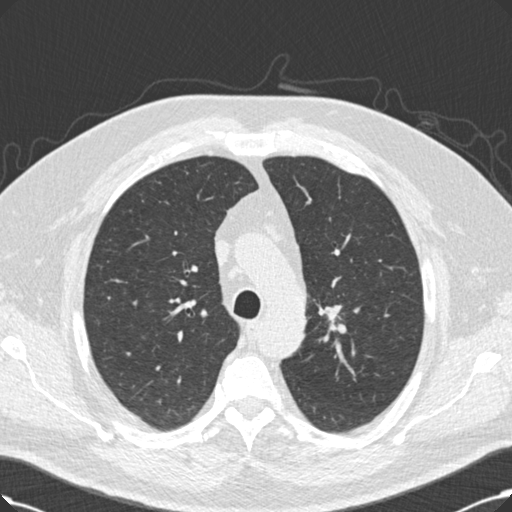
Low-dose screening chest CT, one axial slice; slice 161 of 214 in the series (ordered by position); lung window (W 1500 / L -600 HU); 2 mm slice thickness; 512 × 512 image matrix, field of view 365 × 365 mm.
Structures marked on this image (manually delineated by an expert):
- lesion 1 (tumor): bounding box [x1, y1, x2, y2] px = [319, 305, 342, 331]